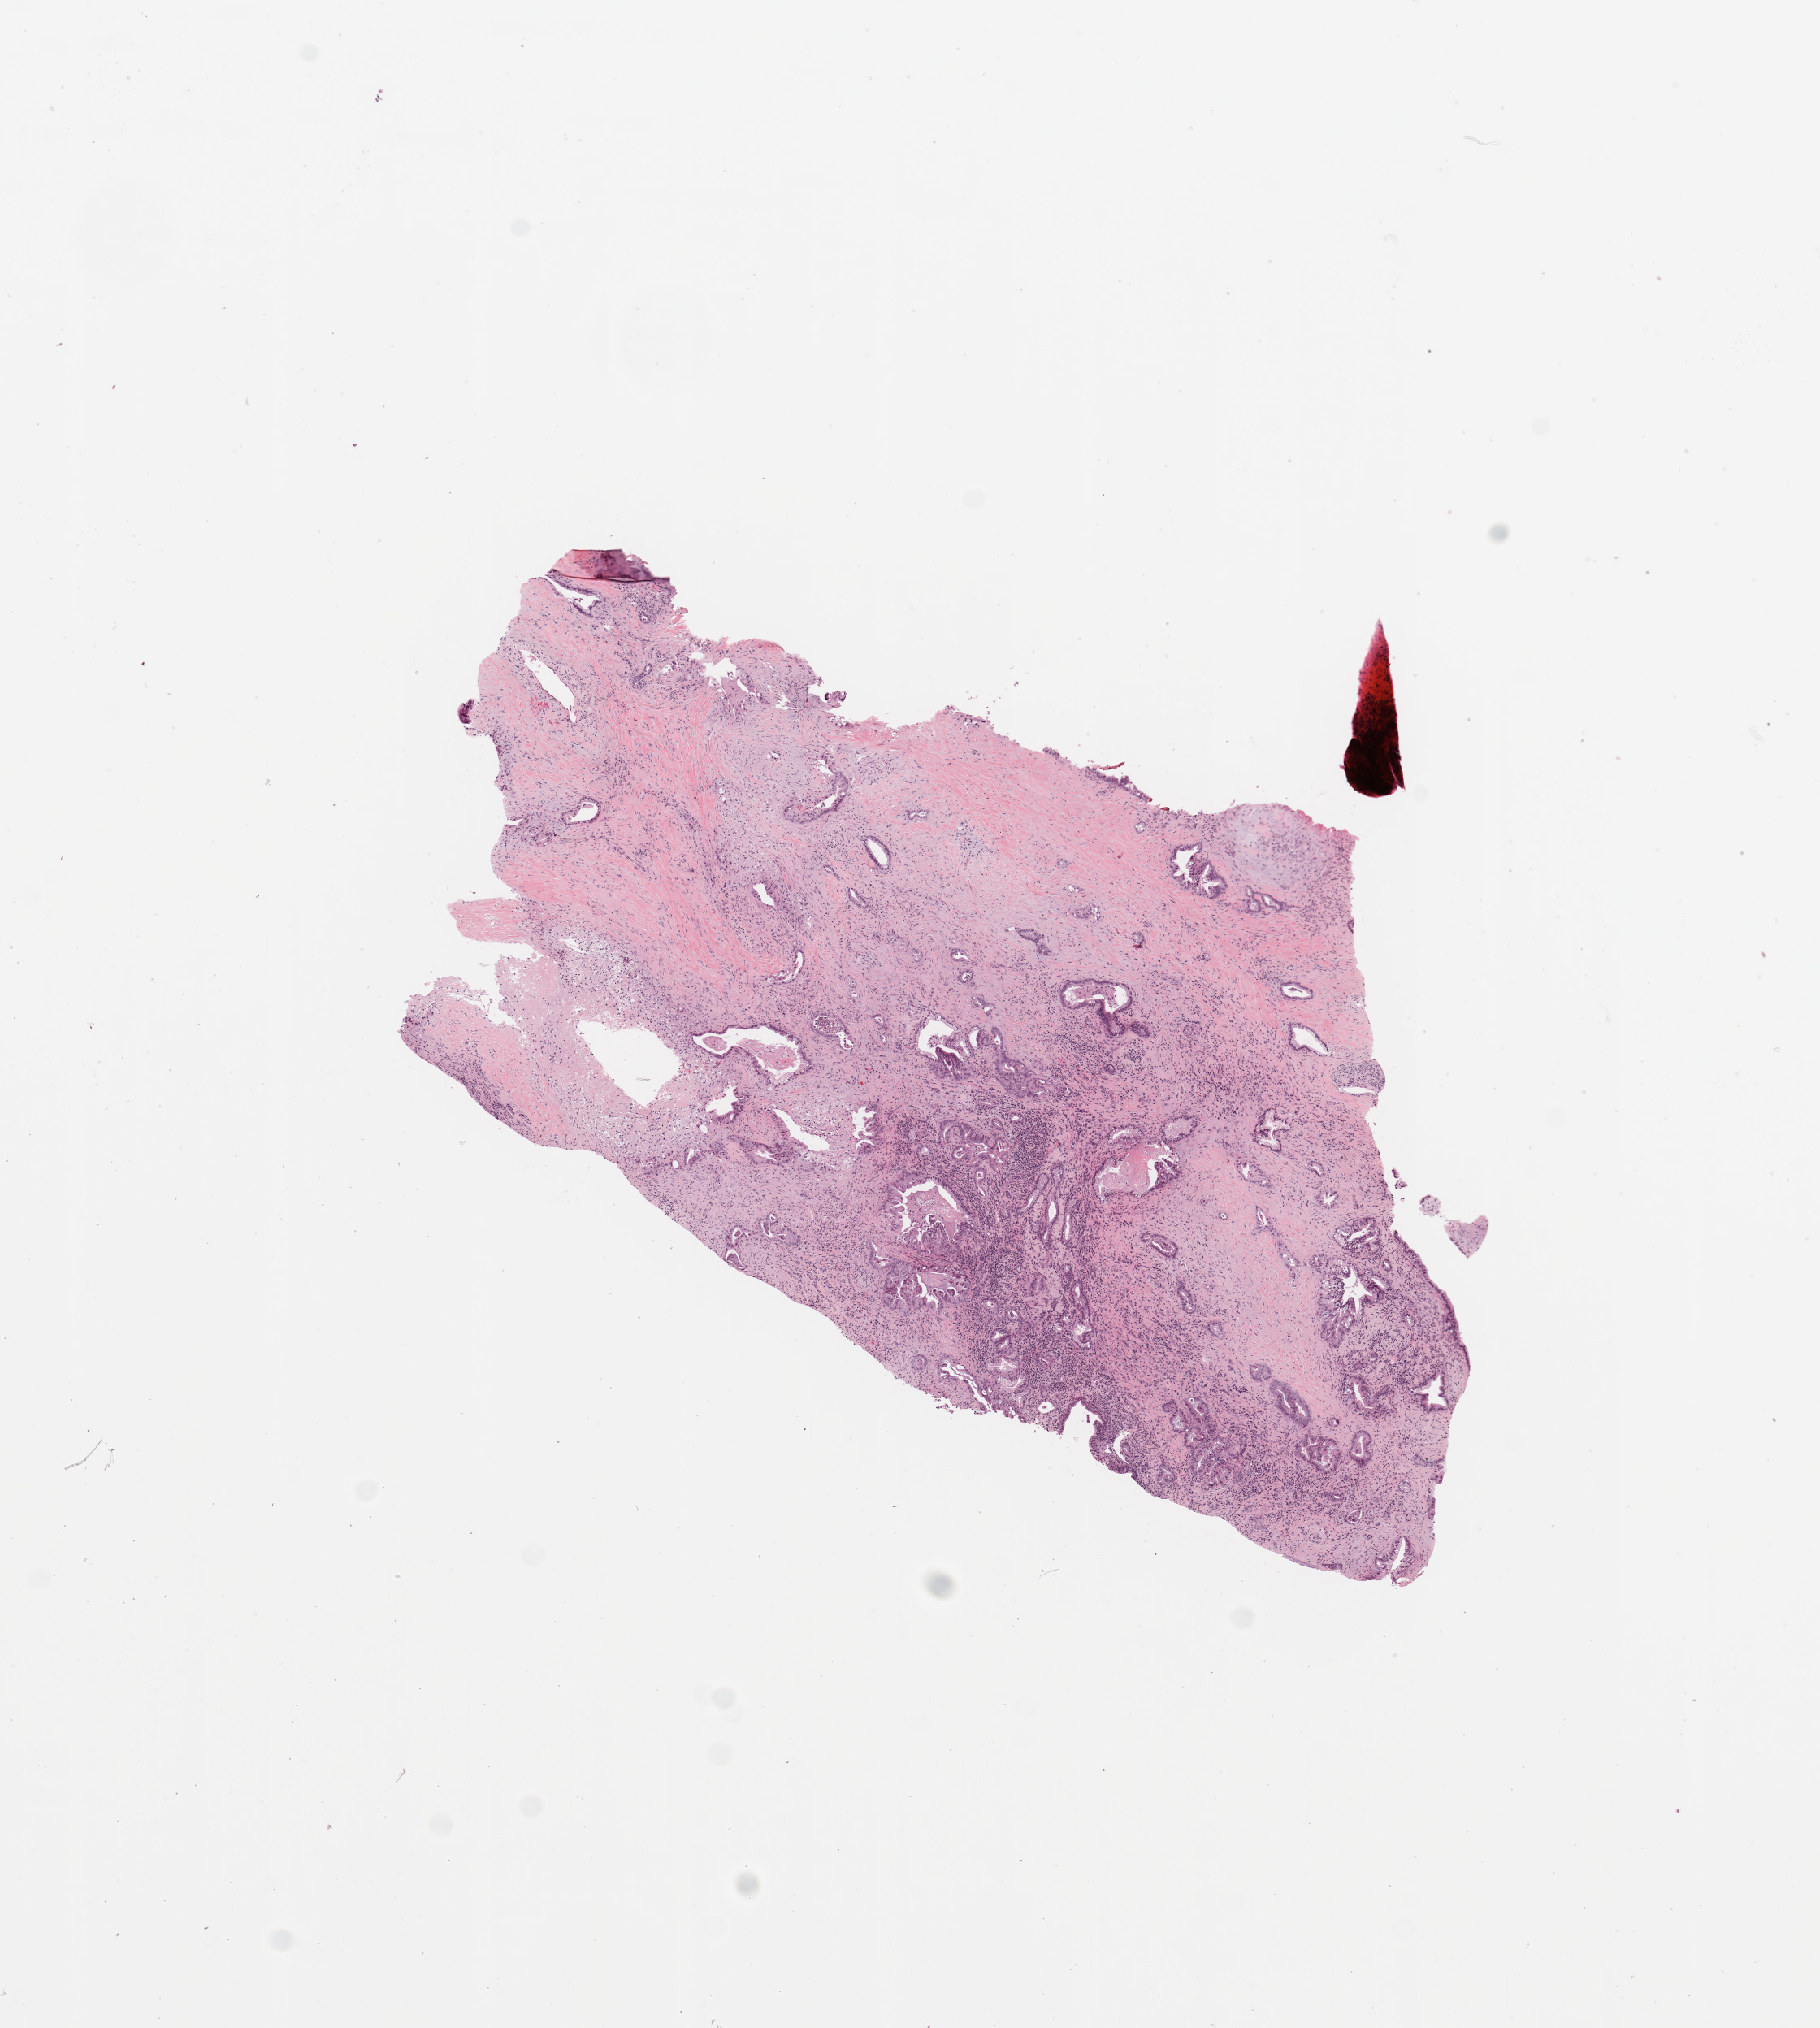
H&E-stained whole-slide image, shown as a low-resolution overview of the whole scanned area (about 8.9 x 9.9 mm, from a 20x scan), tumour tissue sample, pancreas. Patient: female, age 73 years. Histologic grade: G2 (moderately differentiated).
Histologic diagnosis: Infiltrating duct carcinoma, NOS. AJCC pathologic stage: IIB.